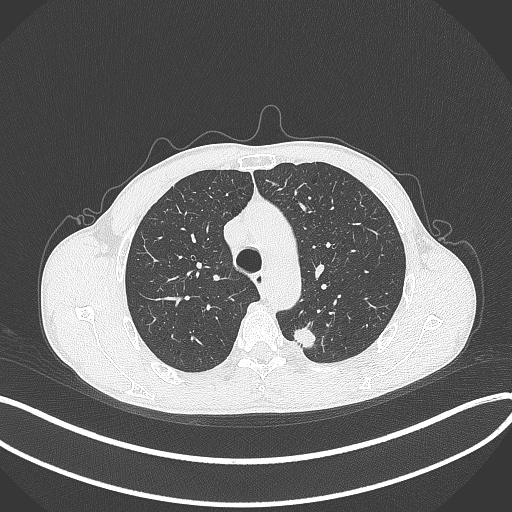
Chest CT, one axial slice. Slice 292 of 429 in the series (ordered by position). Reconstruction kernel B70f. 120 kVp. Lung window (W 1500 / L -600 HU). 512 × 512 image matrix, field of view 400 × 400 mm. Patient: male, 51 years. From the clinical record (not read from this slice): clinical TNM (as recorded): T2a N1 M1.
Annotated regions visible in this slice (rectangle marked by the reading radiologist):
- lung tumour (recorded histology: adenocarcinoma): bounding box [x1, y1, x2, y2] px = [289, 323, 319, 354]